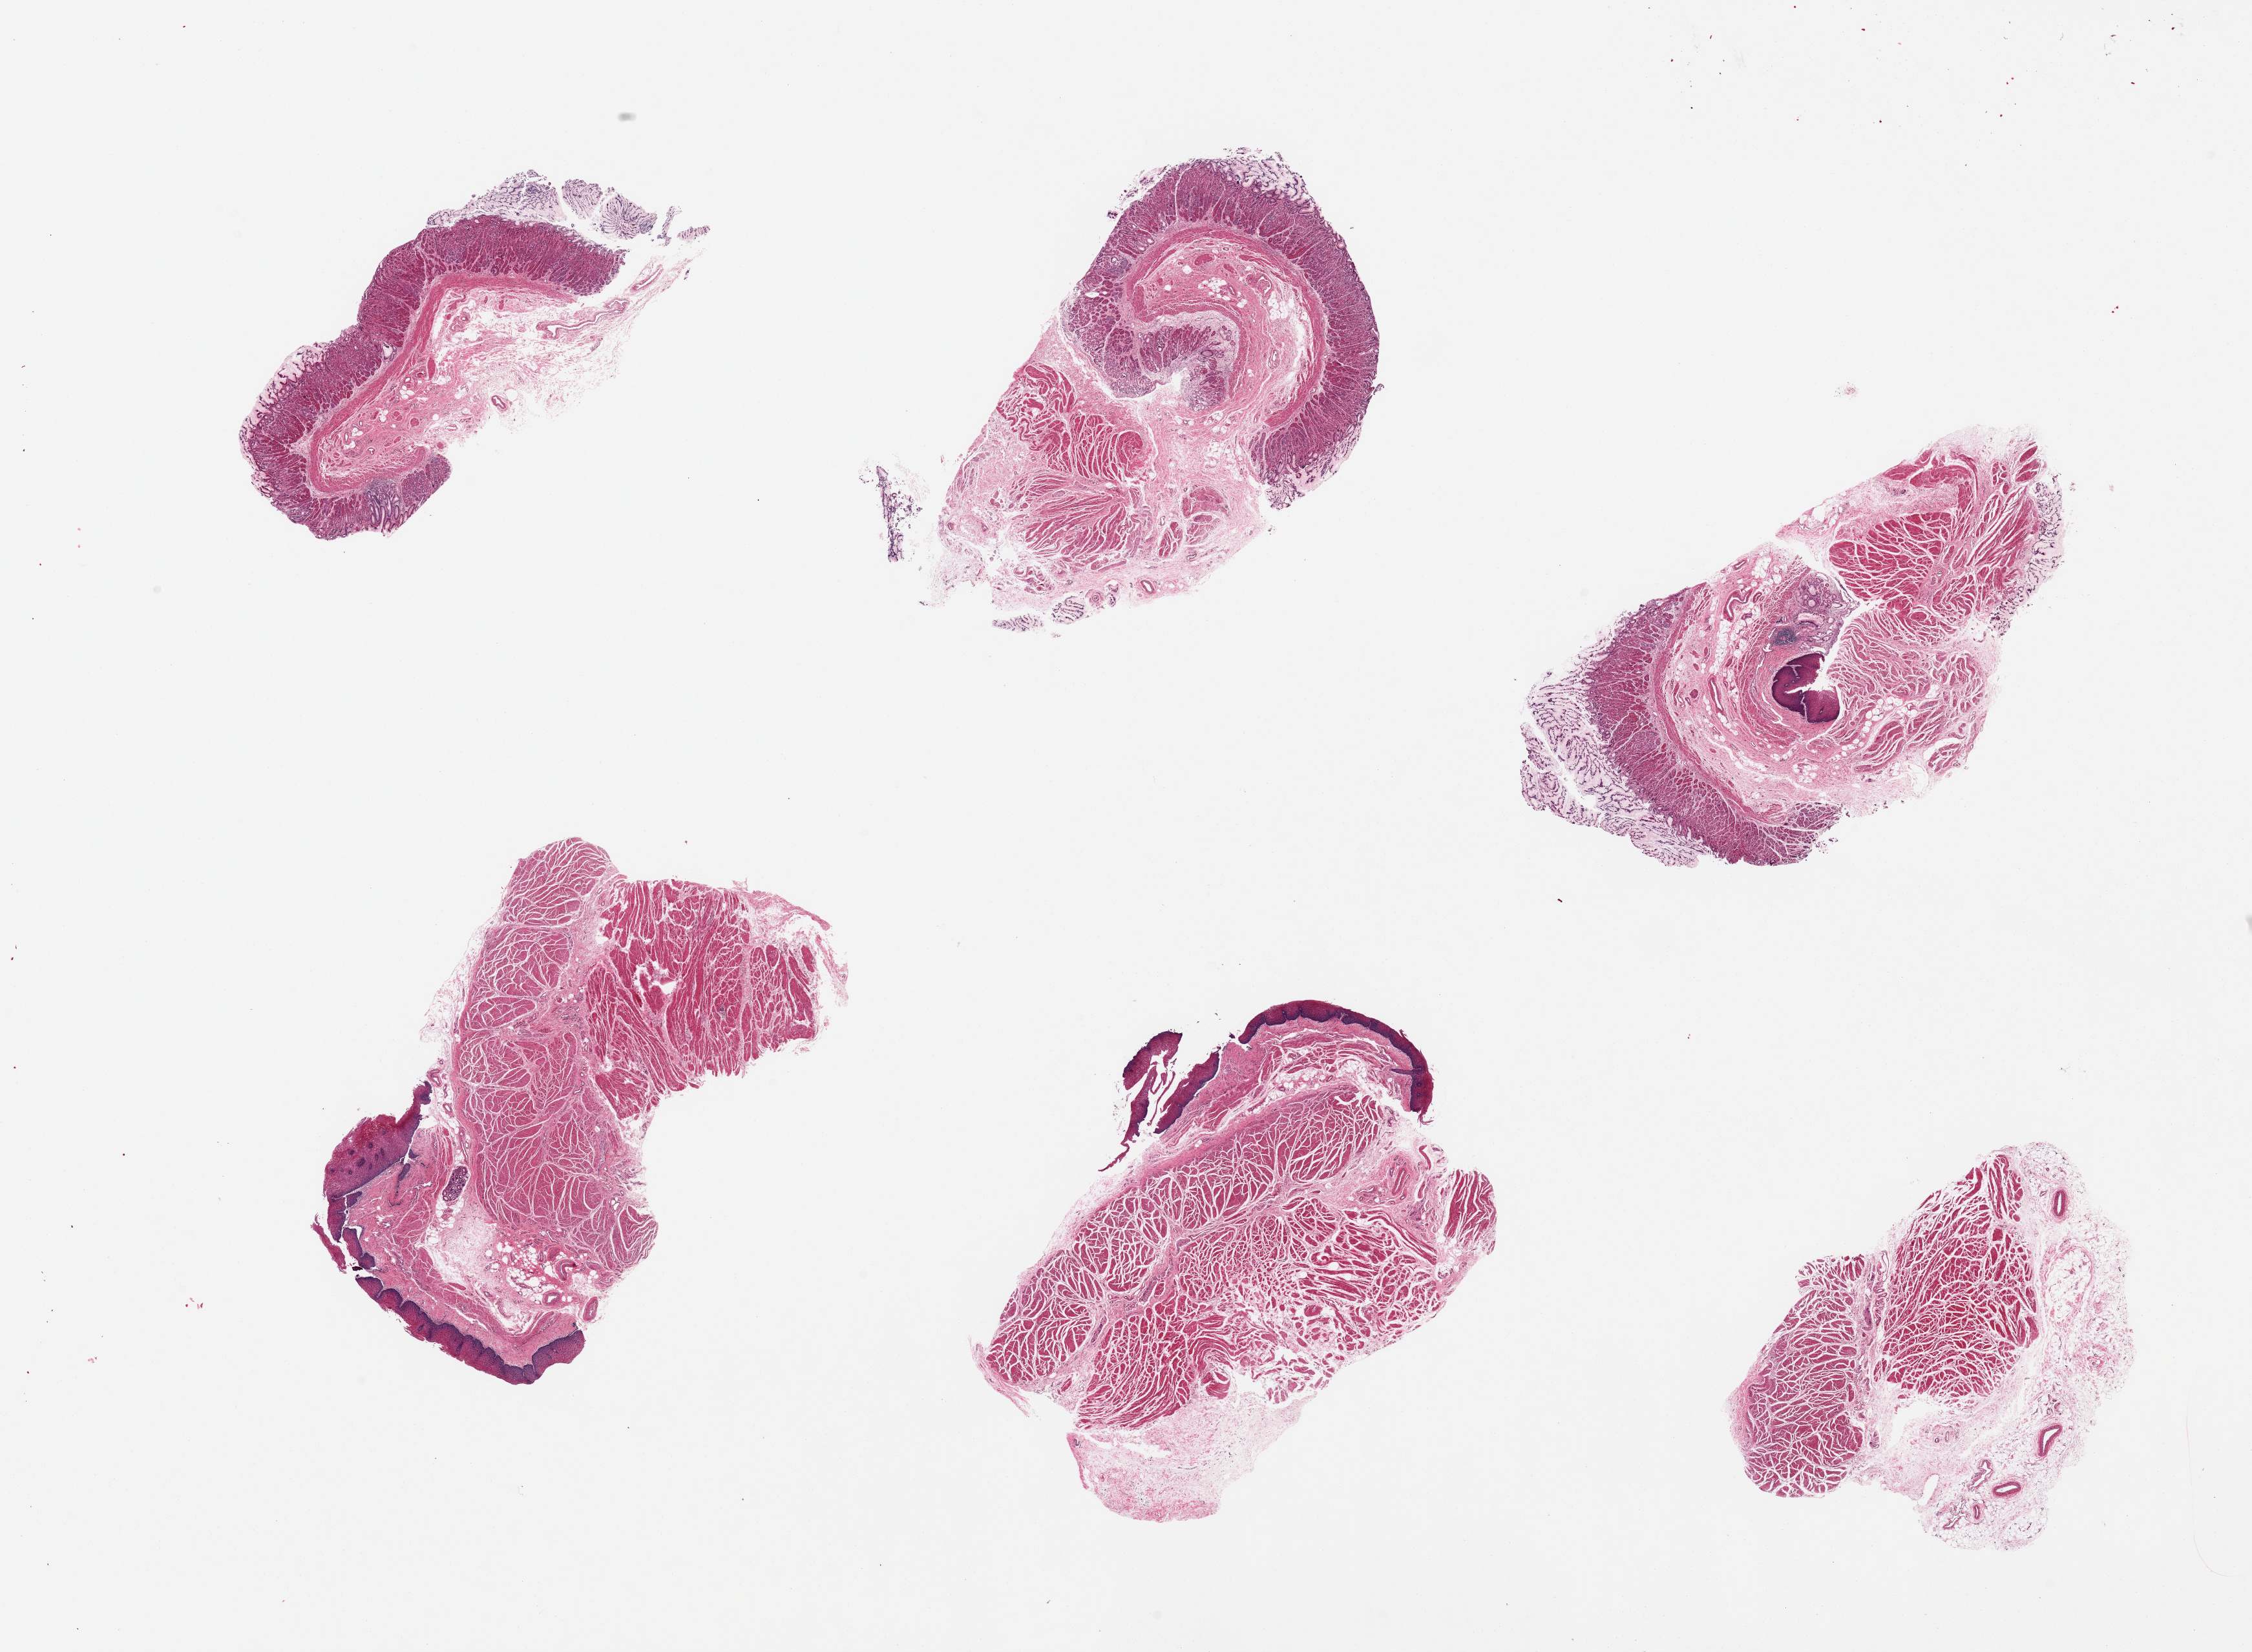
Digitized hematoxylin and eosin (H&E)-stained section, a low-resolution overview of the entire scanned area, about 27.6 x 20.2 mm (slide scanned at 20x); PAXgene-fixed, paraffin-embedded tissue; sampled site (target tissue): gastroesophageal junction; donor tissue sample. Donor sex: male.
Reviewer comment on this tissue sample: 6 pieces, one lacks muscularis (target) and several contain mucosa (not target, squamous and gastric).